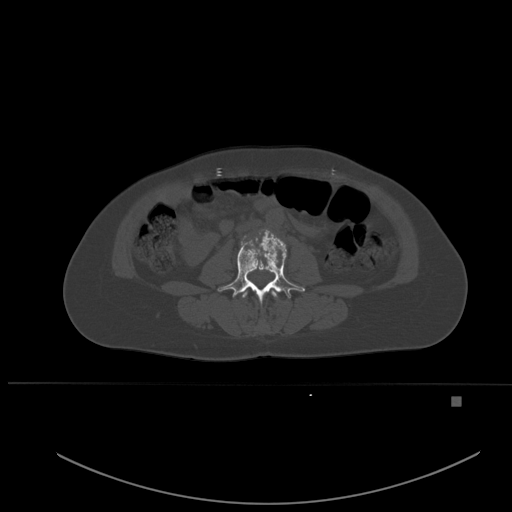
CT including the spine, one axial slice; slice 195 of 651 in the series (ordered by position); bone window (W 1800 / L 400 HU); 512 × 512 image matrix. Patient: female, 49 years. From the clinical record (not read from this slice): primary cancer: breast; vertebrae with lytic lesions (as recorded): L3, T12, L4.
Outlined on this slice (semi-automatically segmented with operator editing):
- L2 vertebra: bounding box <242,290,278,298> (left, top, right, bottom; pixels)
- L3 vertebra: <218,231,305,303>